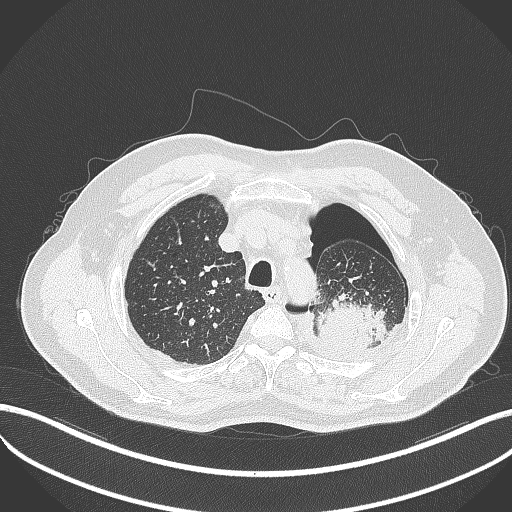
Chest CT, one axial slice; slice 406 of 464 in the series (ordered by position); 120 kVp; lung window (W 1500 / L -600 HU); 1 mm slice thickness; 512 × 512 image matrix. Patient: male, 76 years. From the clinical record (not read from this slice): clinical TNM (as recorded): T3 N0 M1b.
Annotated regions visible in this slice (rectangle marked by the reading radiologist):
- lung tumour (recorded histology: adenocarcinoma): bounding box <311,296,388,350> (left, top, right, bottom; pixels)